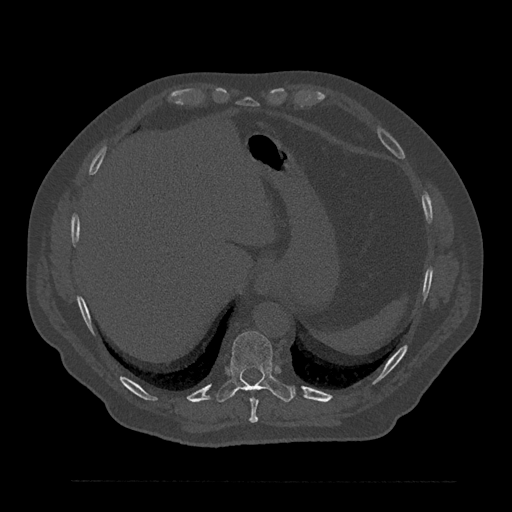
CT including the spine, one axial slice; slice 364 of 797 in the series (ordered by position); reconstruction kernel Br40s/3; 120 kVp; bone window (W 1800 / L 400 HU); 512 × 512 image matrix. Male patient, age 61 years. Case-level facts recorded for this patient, not image findings: primary cancer: prostate.
Outlined on this slice (semi-automatic segmentation, software-assisted and operator-edited):
- T10 vertebra: bounding box <216,331,294,403> (left, top, right, bottom; pixels)
- T9 vertebra: <249,389,259,423>